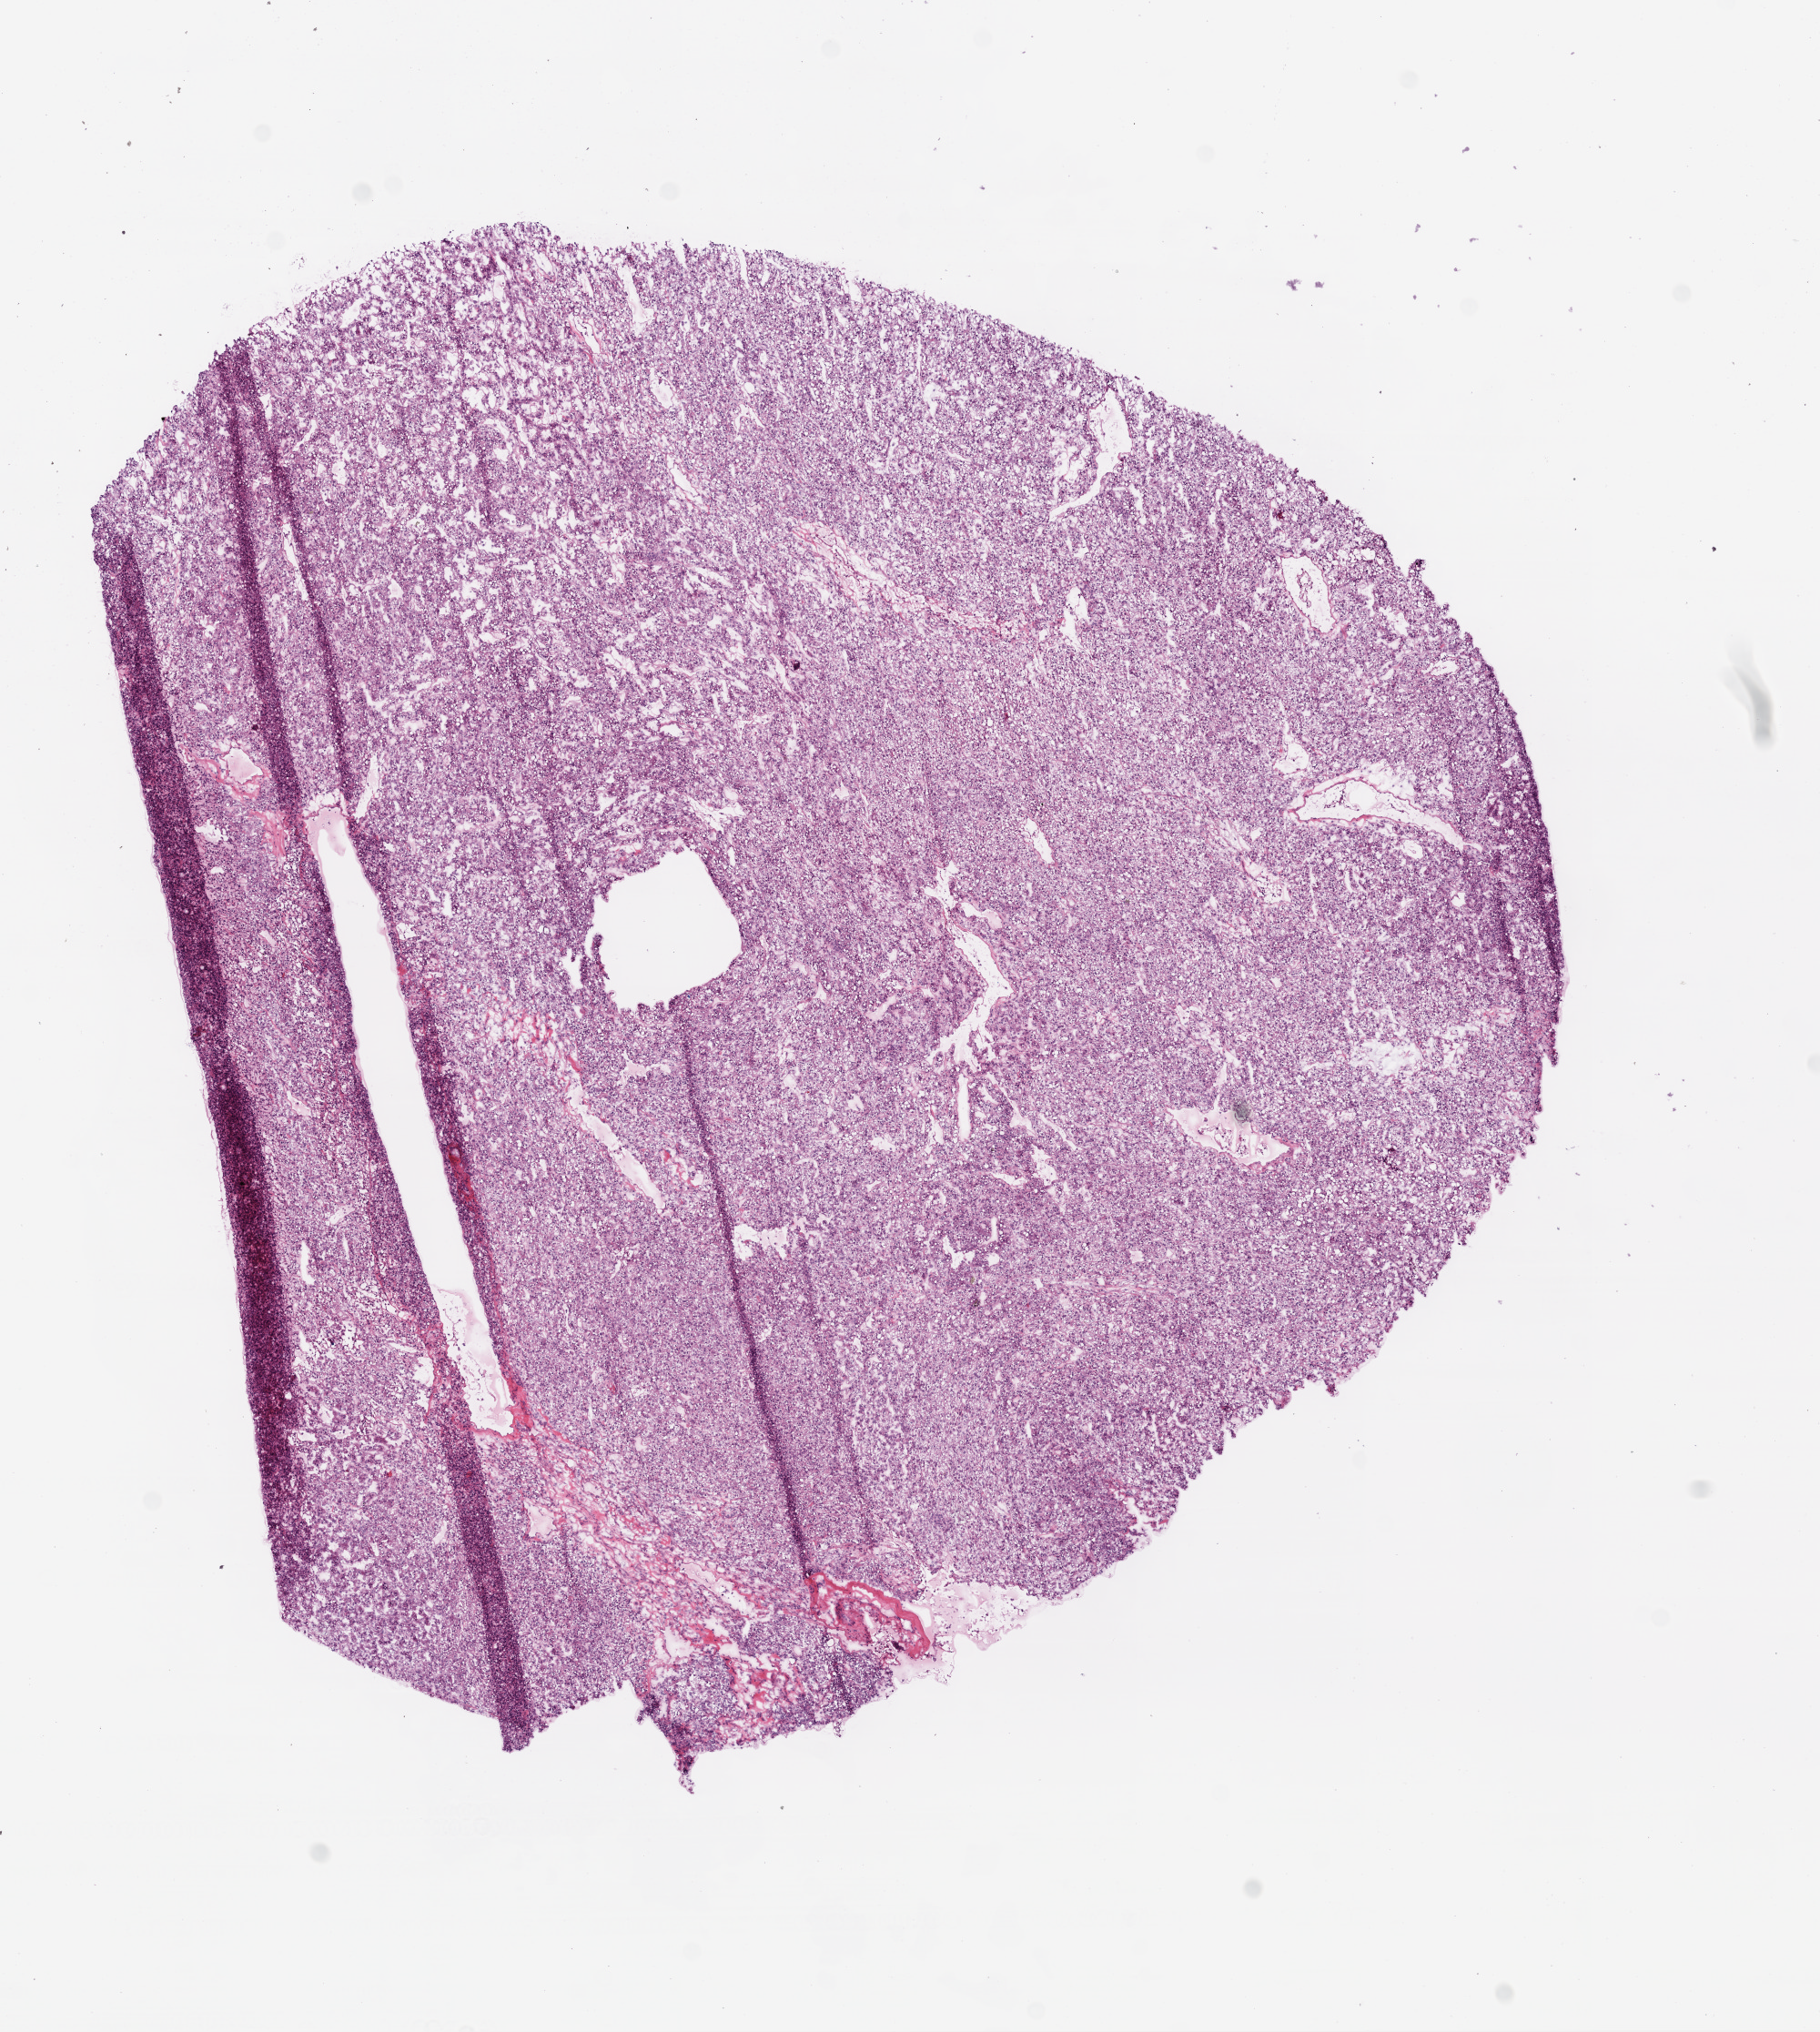
Whole-slide histology image, H&E, low-resolution overview of the scanned area, about 8.0 x 9.0 mm (acquisition: 20x scan); frozen section from the top of the tissue portion; kidney, primary tumour sample. Patient sex: female. Histologic grade: G2 (moderately differentiated). Composition of this section per pathologist review: tumour cells 95%, tumour nuclei 90%, normal cells 0%, stromal cells 5%, necrosis 0%.
* diagnosis: Clear cell adenocarcinoma, NOS
* AJCC pathologic stage: I
* TNM: T1 N0 M0
* laterality: right